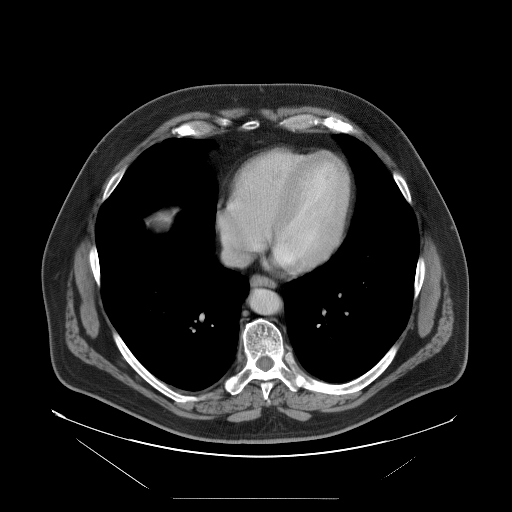
Contrast-enhanced abdominal CT, one axial slice. Slice 101 of 114 in the series (ordered by position). Intravenous contrast given. Soft-tissue window (W 400 / L 40 HU). 5 mm slice thickness. 512 × 512 image matrix. Male patient, age 61 years. From the clinical record (not read from this slice): diagnosis: colorectal cancer liver metastases, imaged before liver resection; multiple liver metastases: no; largest metastasis: 6.5 cm; disease in both lobes: yes.
Outlined on this slice (outlined manually by an expert reader):
- hepatic veins: box from (x=219, y=214) to (x=268, y=264) px